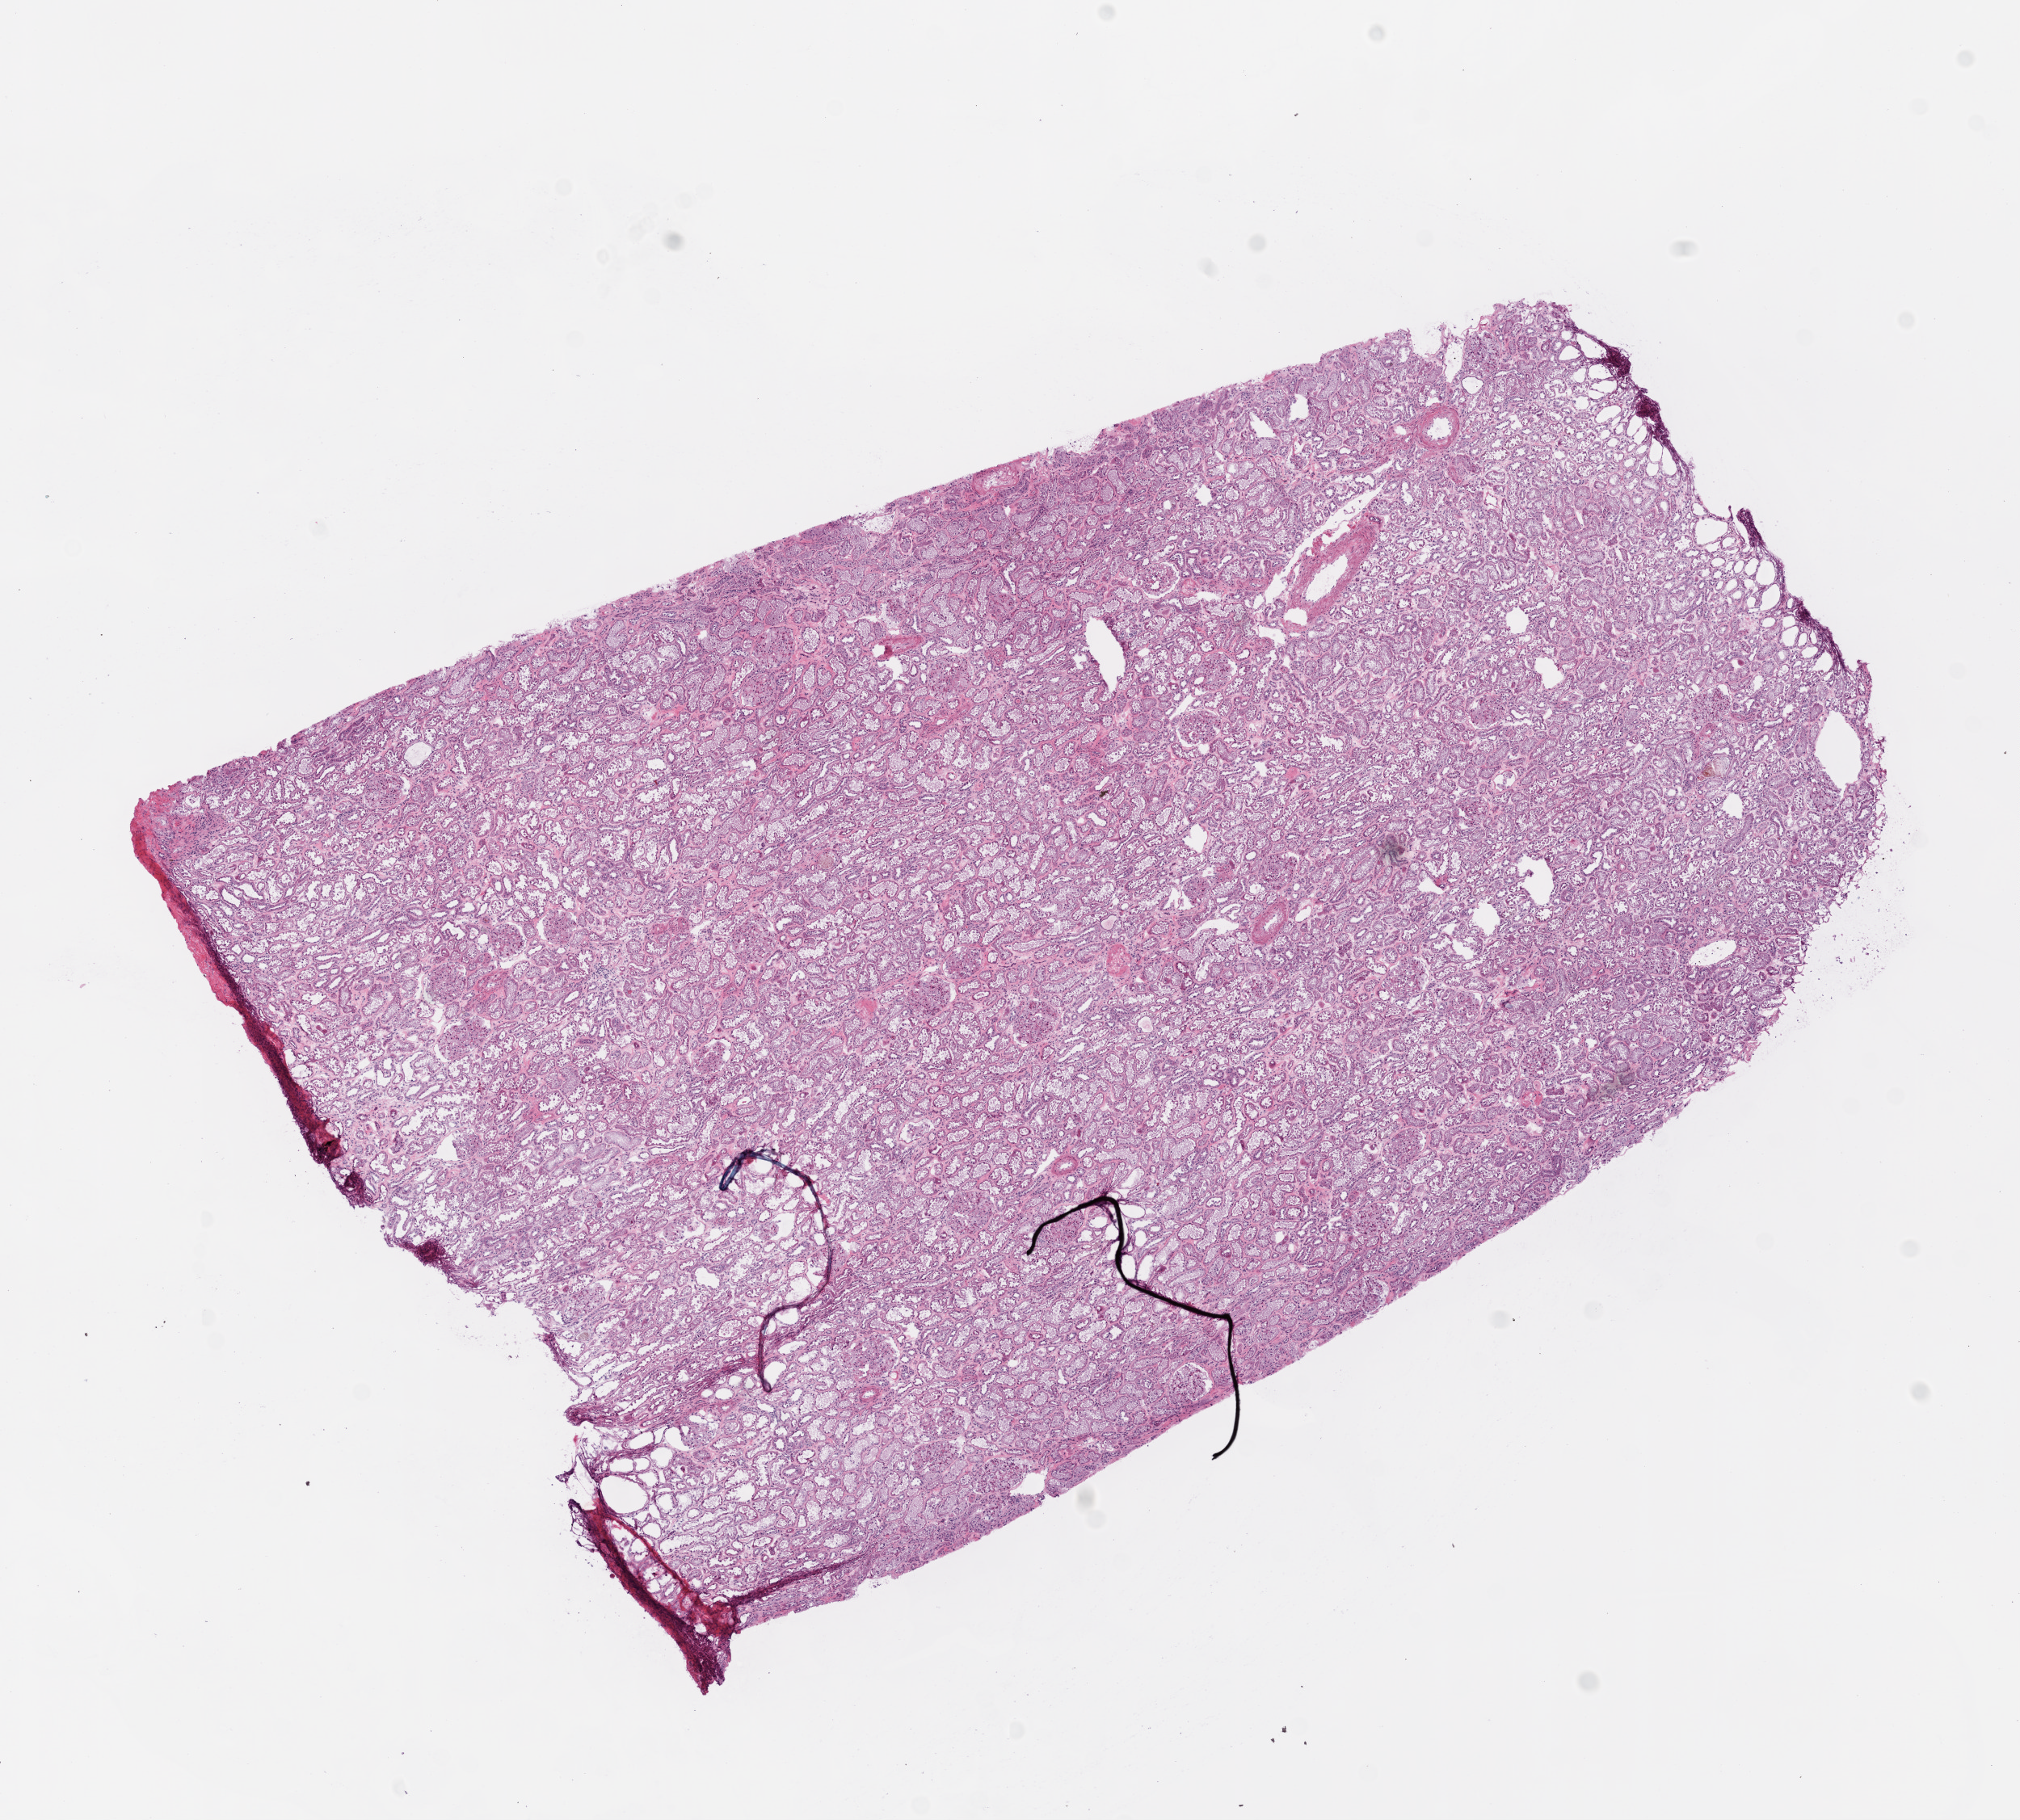
Hematoxylin and eosin (H&E) stained whole-slide image — low-resolution overview of the scanned area, about 10.0 x 9.0 mm (from a 20x scan); frozen section; sample: solid tissue normal (non-tumour tissue), kidney. Male patient; age at initial diagnosis 70 years.
This section: solid tissue normal sample (biorepository sample class). Patient diagnosis: Clear cell adenocarcinoma, NOS.